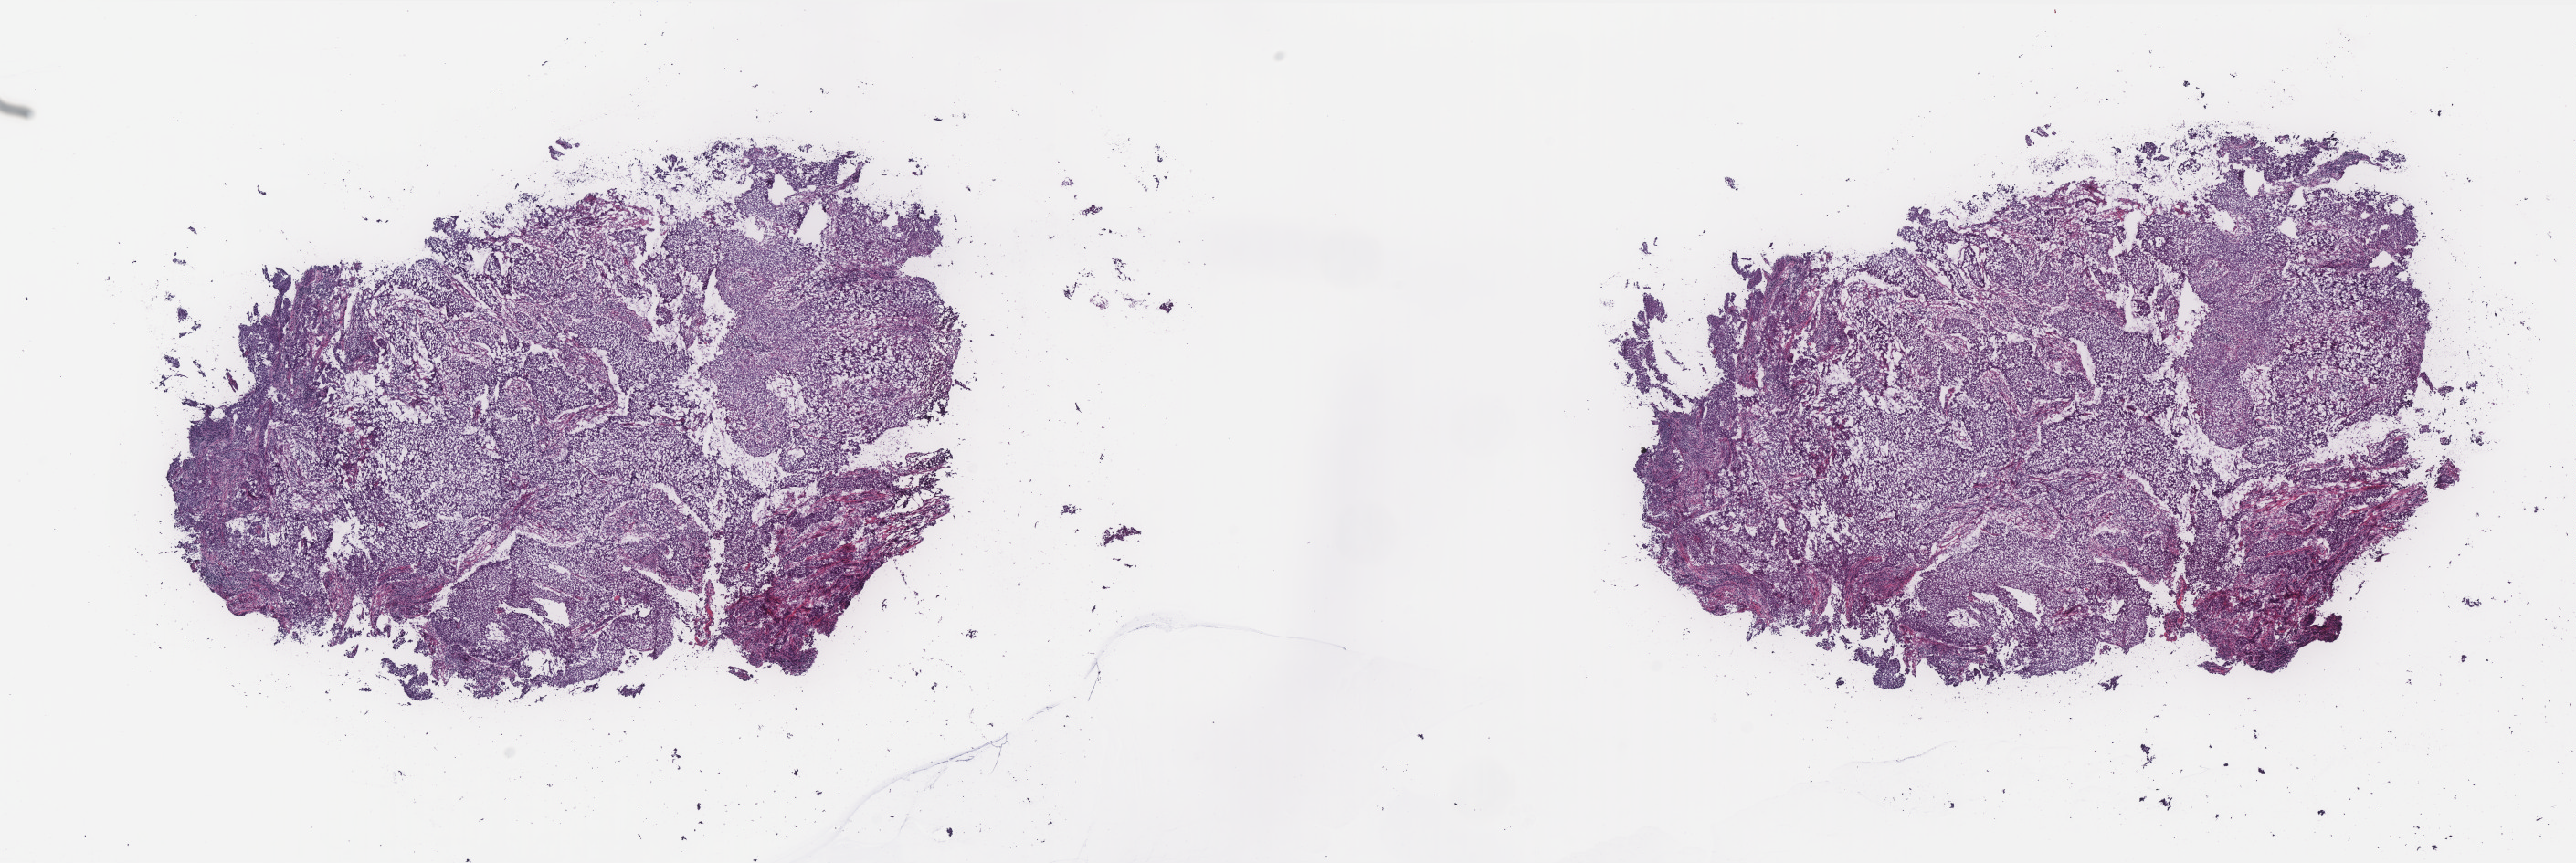
Digitized H&E tissue section (whole slide) — whole scanned area (about 22.6 x 7.6 mm) shown as a low-resolution overview. Frozen section. Cervix, primary tumour sample. Female, age 49 years at initial diagnosis. Histologic grade: G2 (moderately differentiated). Pathologist review of this section (percent, as recorded): tumour cells 78%, tumour nuclei 80%, normal cells 0%, stromal cells 20%, necrosis 2%. Inflammatory infiltration, as recorded: lymphocyte infiltration 30%, monocyte infiltration 10%, neutrophil infiltration 3%.
FIGO stage: IB2. Diagnosis: Squamous cell carcinoma, NOS (cervix uteri).